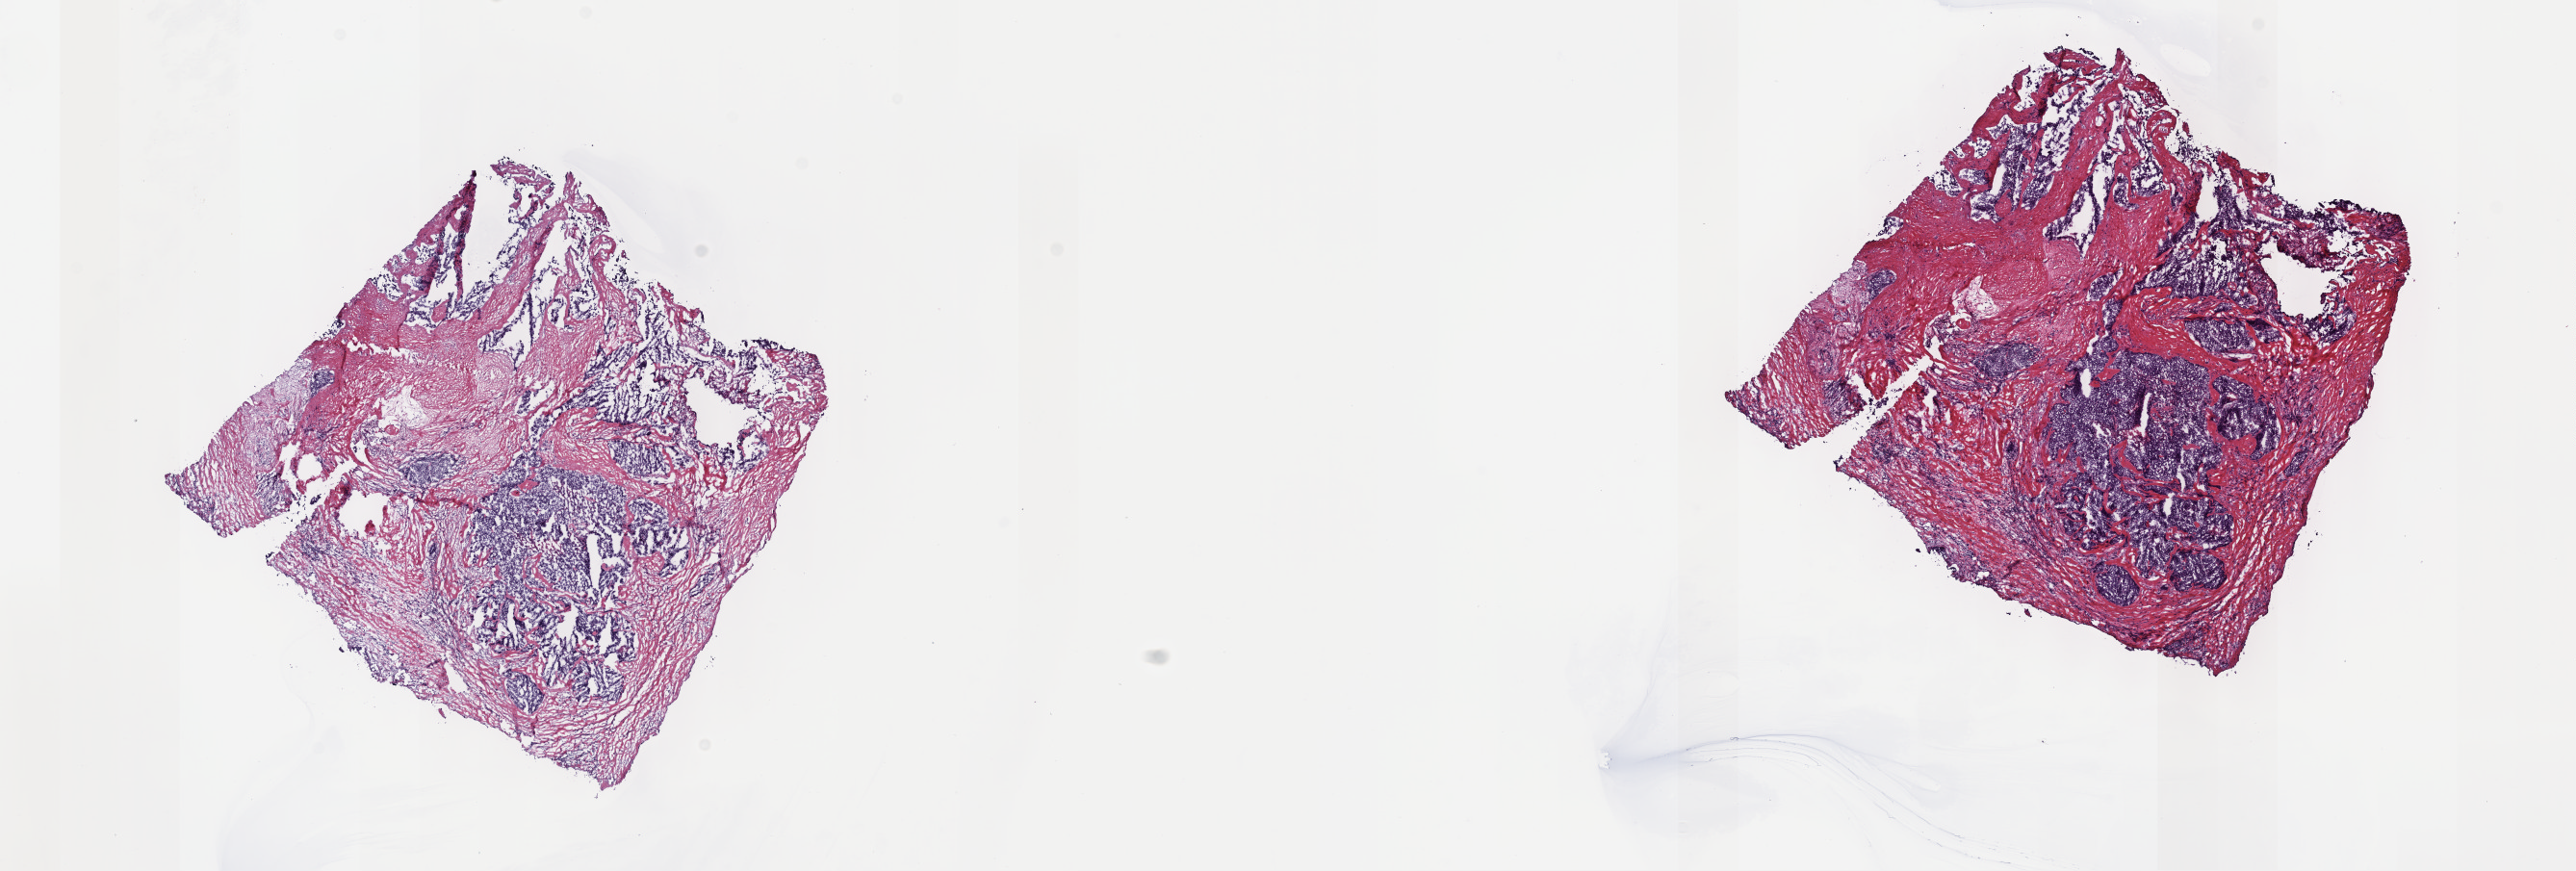
Whole-slide histology image, H&E — shown as a low-resolution overview of the whole scanned area (about 21.6 x 7.3 mm, slide scanned at 40x), frozen section from the top of the tissue portion, primary tumour sample from the thymus. Female, age 52 years at initial diagnosis. Composition of this section per pathologist review: tumour cells 35%, tumour nuclei 60%, normal cells 0%, stromal cells 65%, necrosis 0%. Inflammatory infiltration, as recorded: lymphocyte infiltration 2%, monocyte infiltration 0%, neutrophil infiltration 0%.
* pathologic diagnosis: Thymic carcinoma, NOS